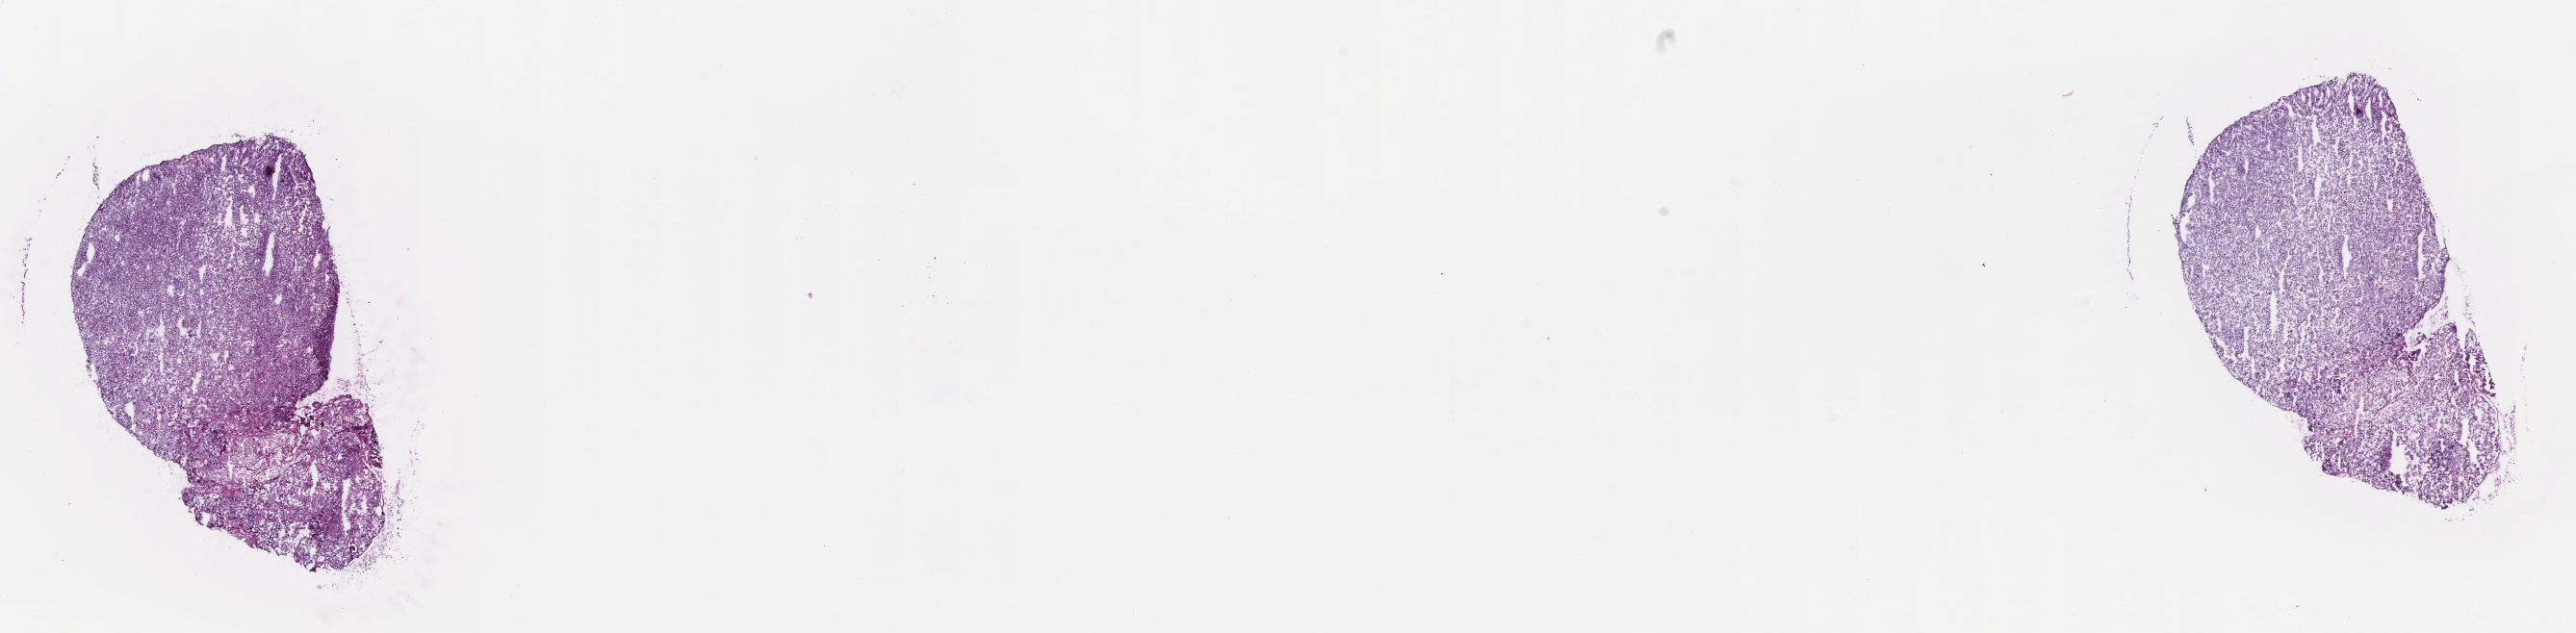
H&E whole-slide image, whole scanned area (about 21.6 x 5.3 mm) shown as a low-resolution overview; cryosection; specimen: primary tumor; anatomic site: cranium. Patient: male, age at initial diagnosis 5 years. Slide review estimates, as recorded: tumor cells 85%, tumor nuclei 85%.
Diagnosis: Burkitt lymphoma, NOS.